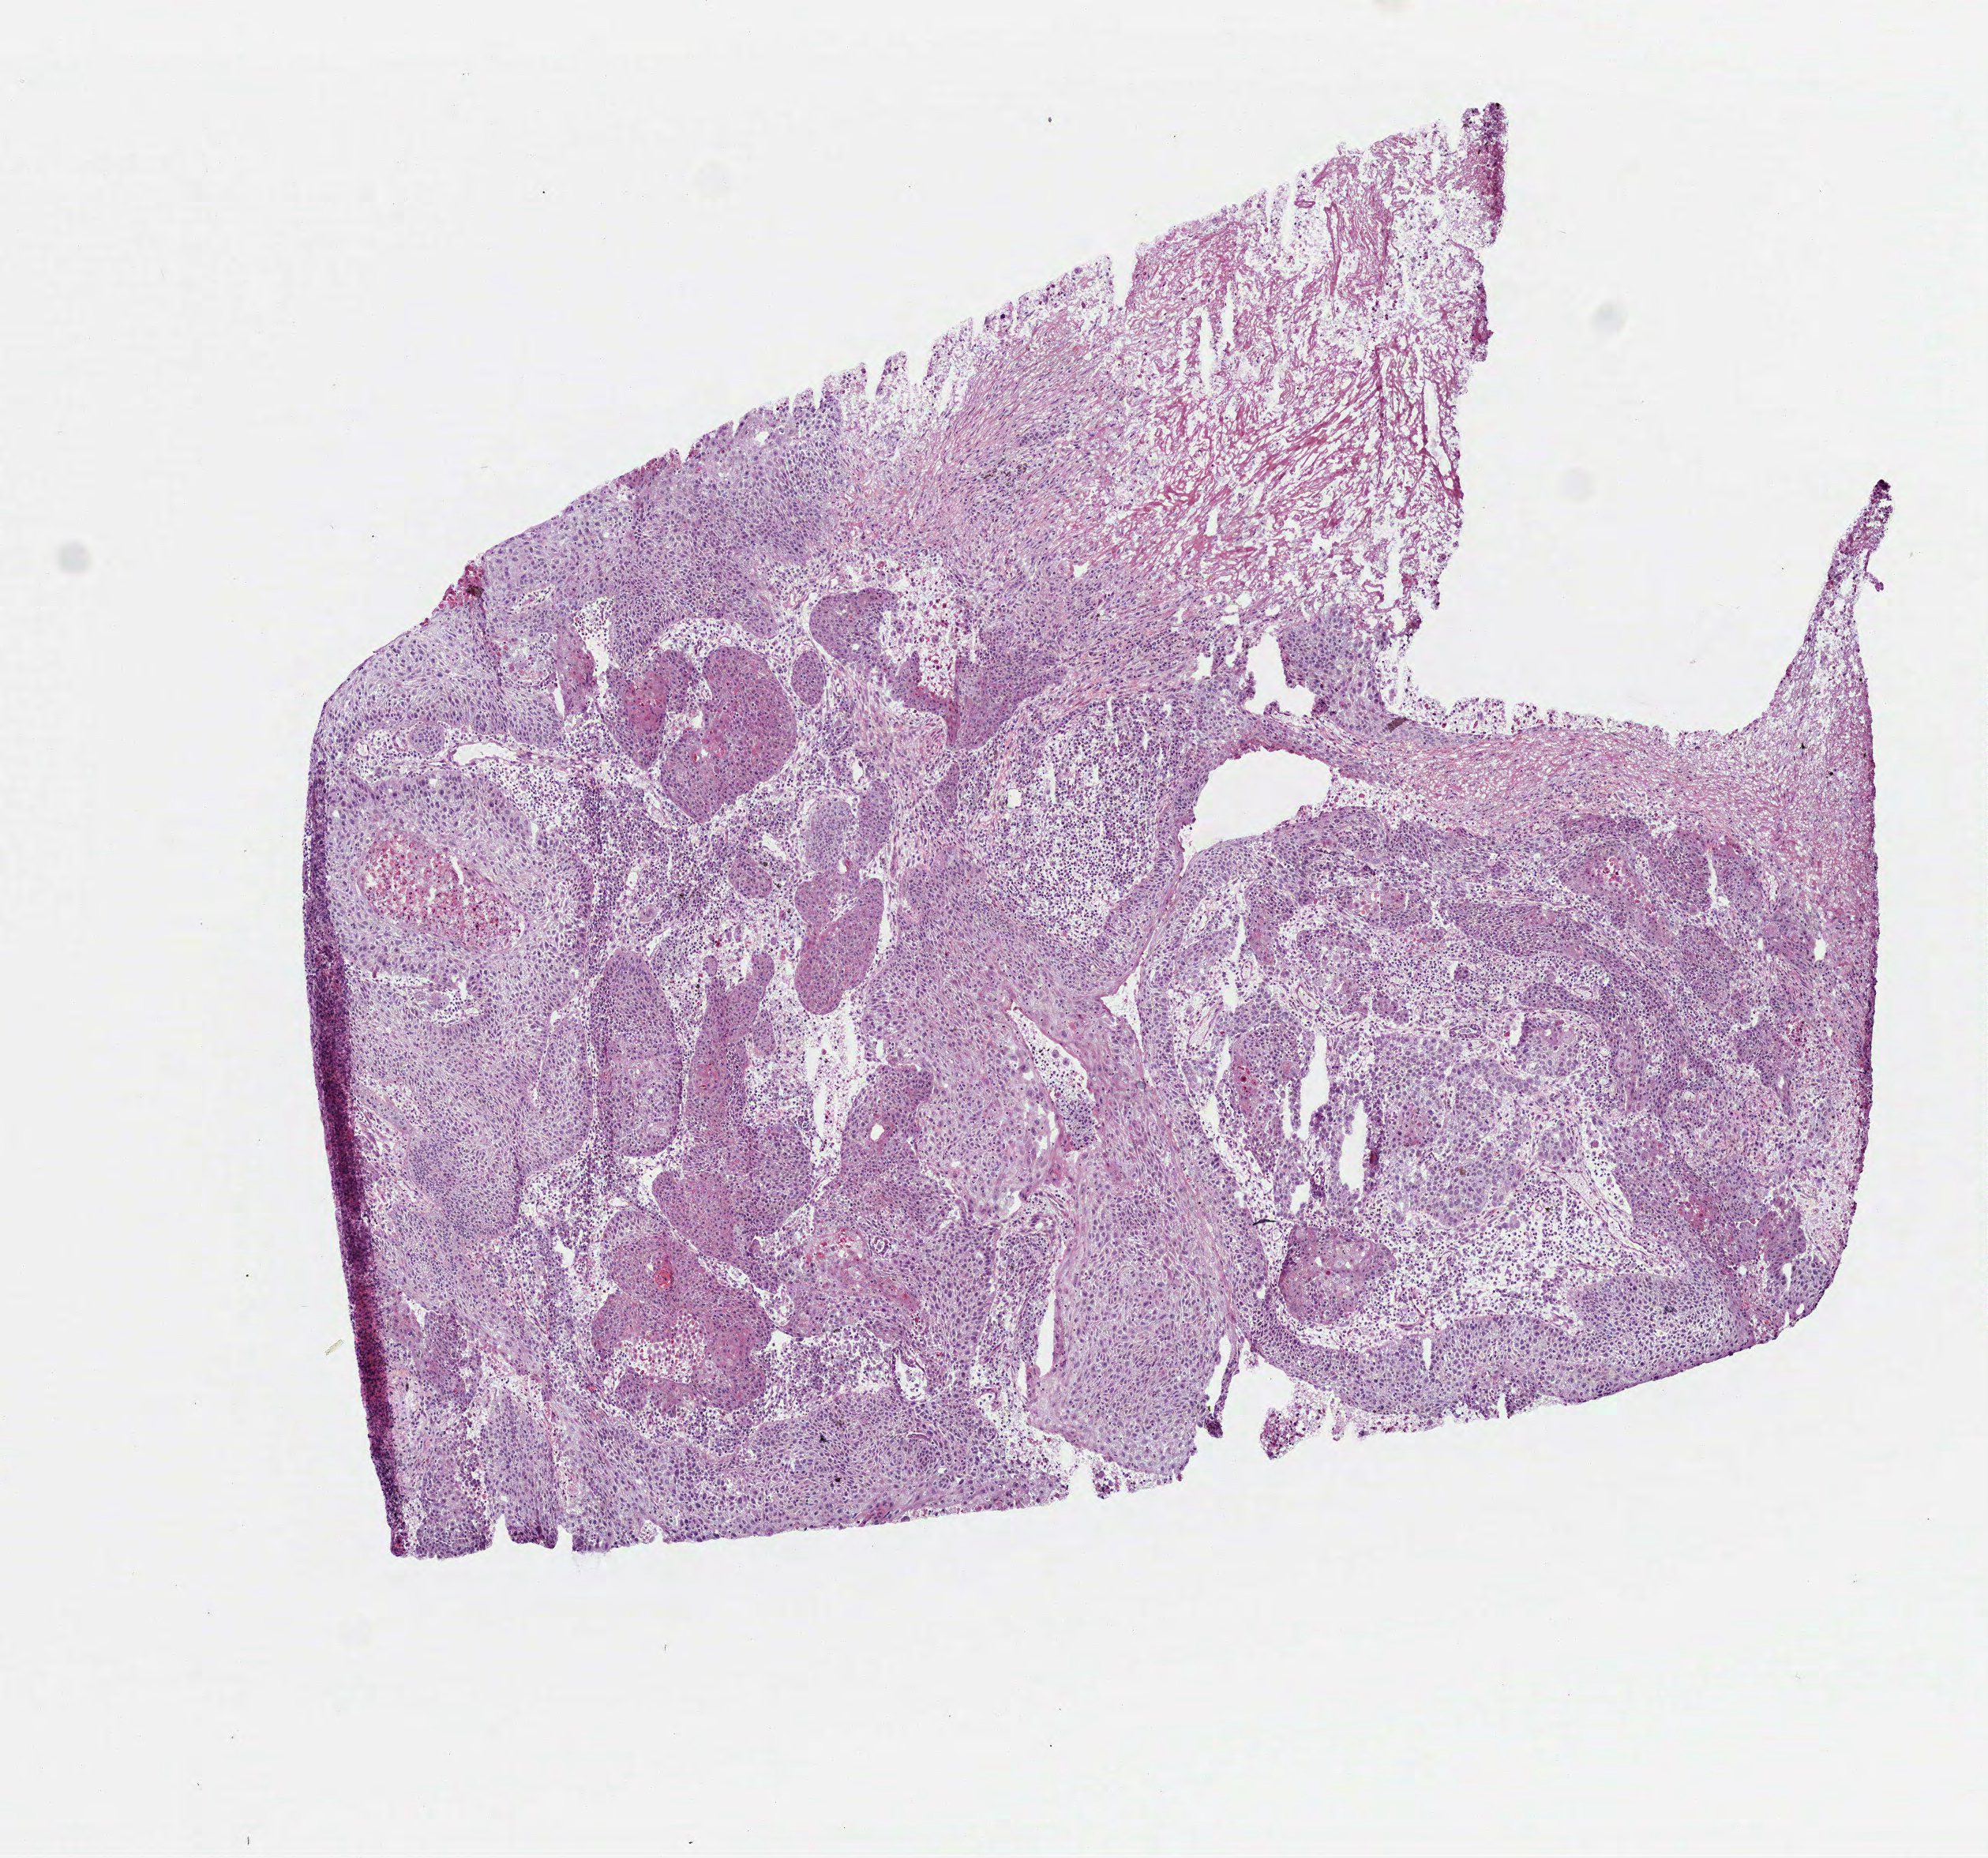
Whole-slide histology image, H&E, shown as a low-resolution overview of the whole scanned area (about 5.1 x 4.7 mm); frozen section; sample: primary tumour, lung. Patient sex: male. Pathologist review of this section (percent, as recorded): tumour cells 98%, tumour nuclei 60%, normal cells 0%, stromal cells 0%, necrosis 2%. Infiltration values recorded for this section: lymphocyte infiltration 20%, monocyte infiltration 10%, neutrophil infiltration 5%.
- AJCC pathologic stage: IA (6th edition)
- histologic diagnosis: Squamous cell carcinoma, NOS (upper lobe, lung)